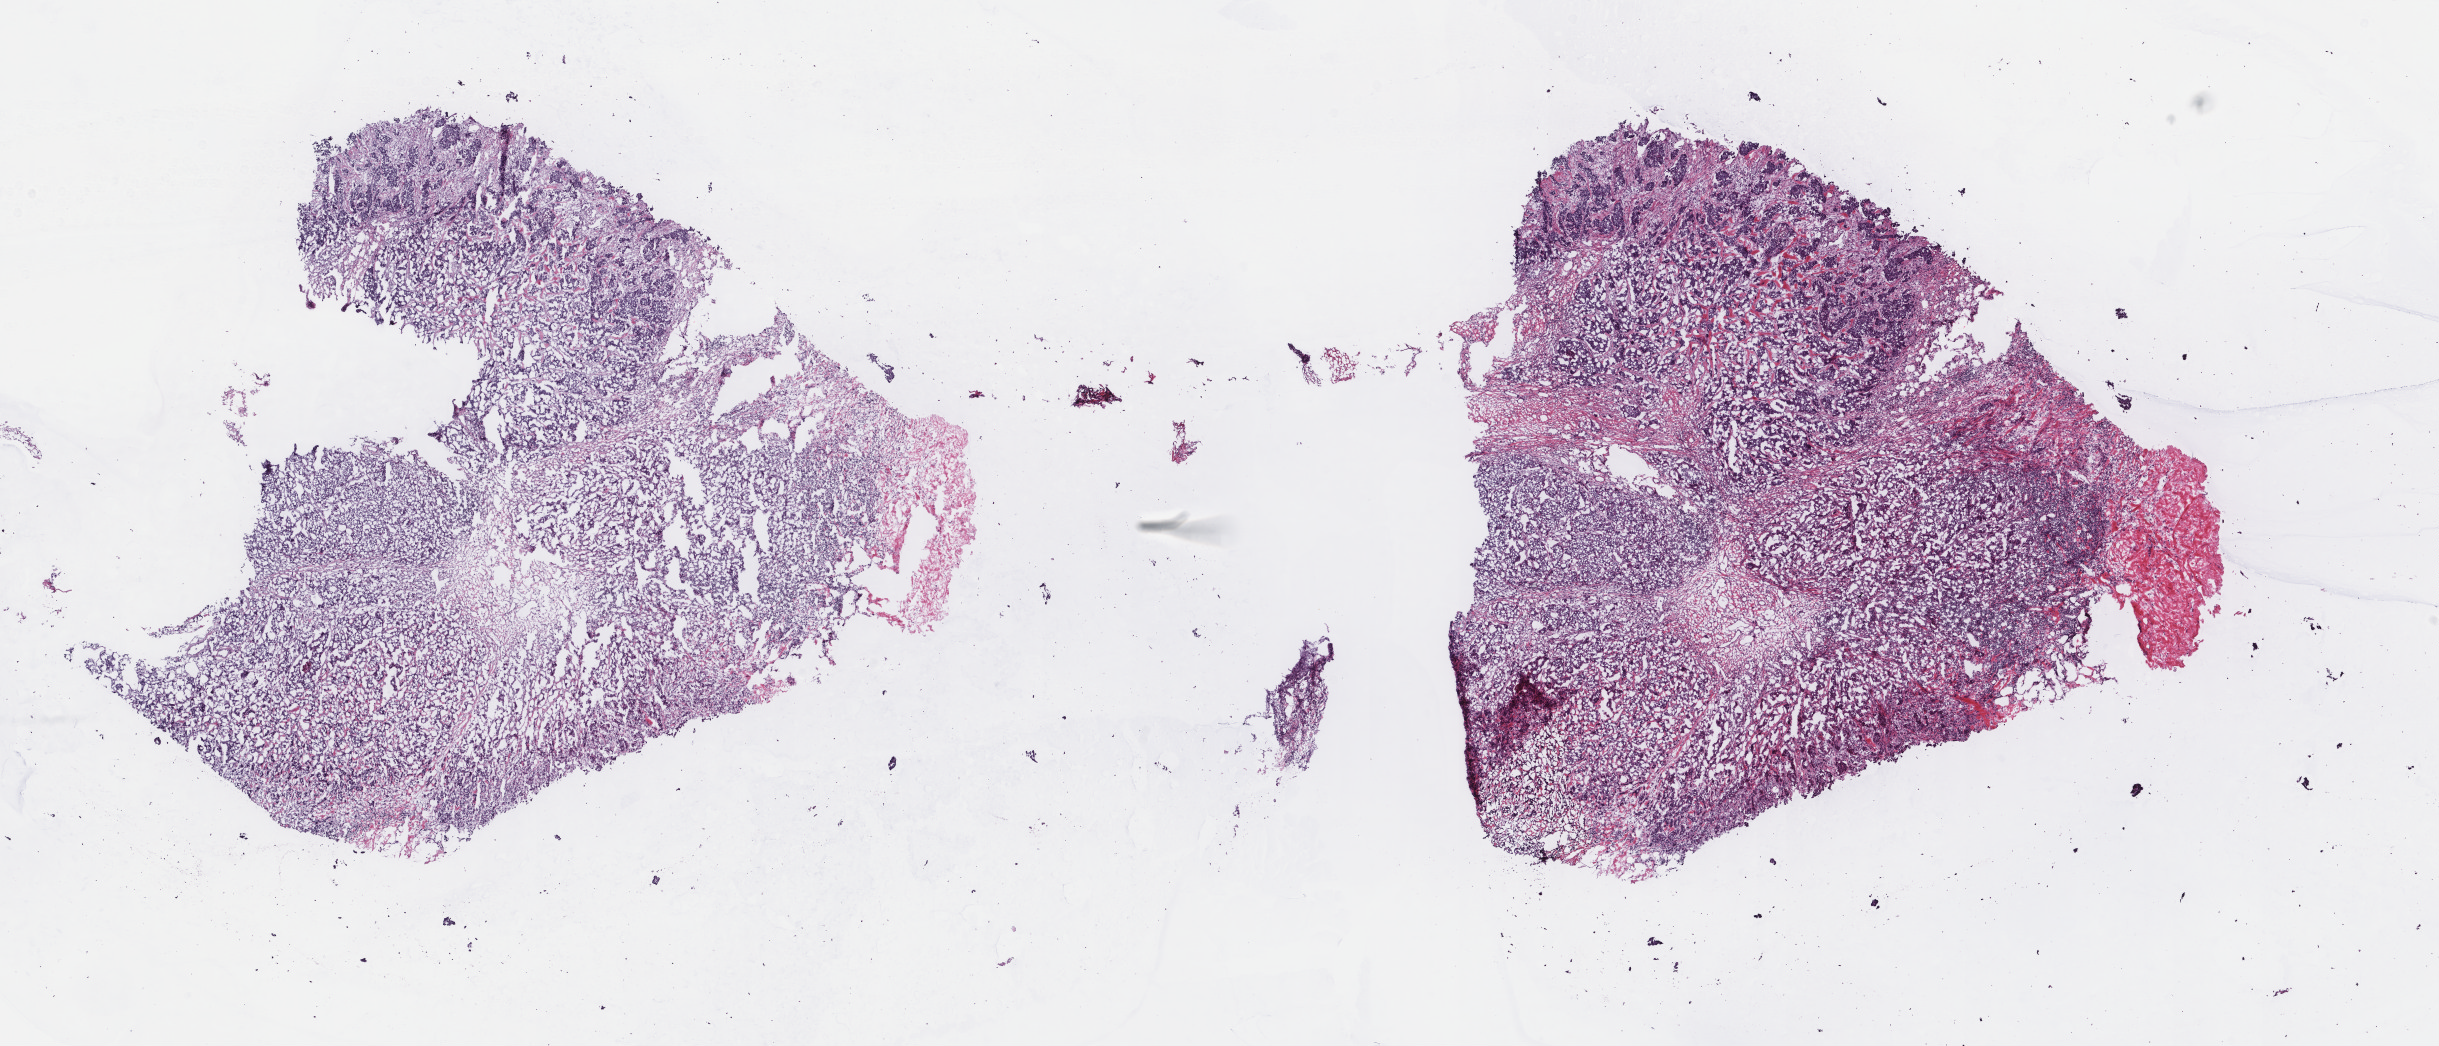
Hematoxylin and eosin (H&E) stained whole-slide image — a low-resolution overview of the entire scanned area, about 19.4 x 8.3 mm. Frozen section. Primary tumour sample from the breast. Male patient; age at initial diagnosis 84 years. Pathologist review of this section (percent, as recorded): tumour cells 80%, tumour nuclei 90%, normal cells 0%, stromal cells 20%, necrosis 0%. Inflammatory infiltration, as recorded: lymphocyte infiltration 0%, monocyte infiltration 0%, neutrophil infiltration 0%.
Lymph nodes positive (case pathology): 2 of 9 examined. Diagnosis: Infiltrating duct carcinoma, NOS. AJCC pathologic stage: IIIB (6th edition).